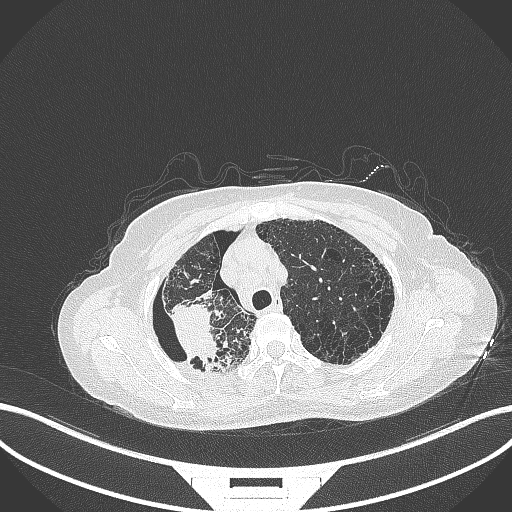
Chest CT, one axial slice; slice 279 of 408 in the series (ordered by position); reconstruction kernel B70f; lung window (W 1500 / L -600 HU); 512 × 512 image matrix, field of view 400 × 400 mm. Patient: female, 64 years. Case-level facts recorded for this patient, not image findings: clinical TNM (as recorded): T3 N3 M0.
Structures marked on this image (bounding box drawn by a radiologist):
- lung tumour (recorded histology: squamous cell carcinoma): bounding box (x1, y1, x2, y2) in pixels: (167, 299, 230, 368)